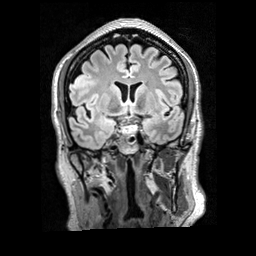
Brain MRI from a brain-tumour surgery series, one coronal slice; slice 117 of 200 in the series (ordered by position); T2 FLAIR; 256 × 256 image matrix. Case-level facts recorded for this patient, not image findings: histopathology: Glioblastoma; WHO grade: 4; IDH mutation: no.
Outlined on this slice (manually delineated by an expert):
- tumour: bounding box [x1, y1, x2, y2] px = [69, 72, 95, 89]